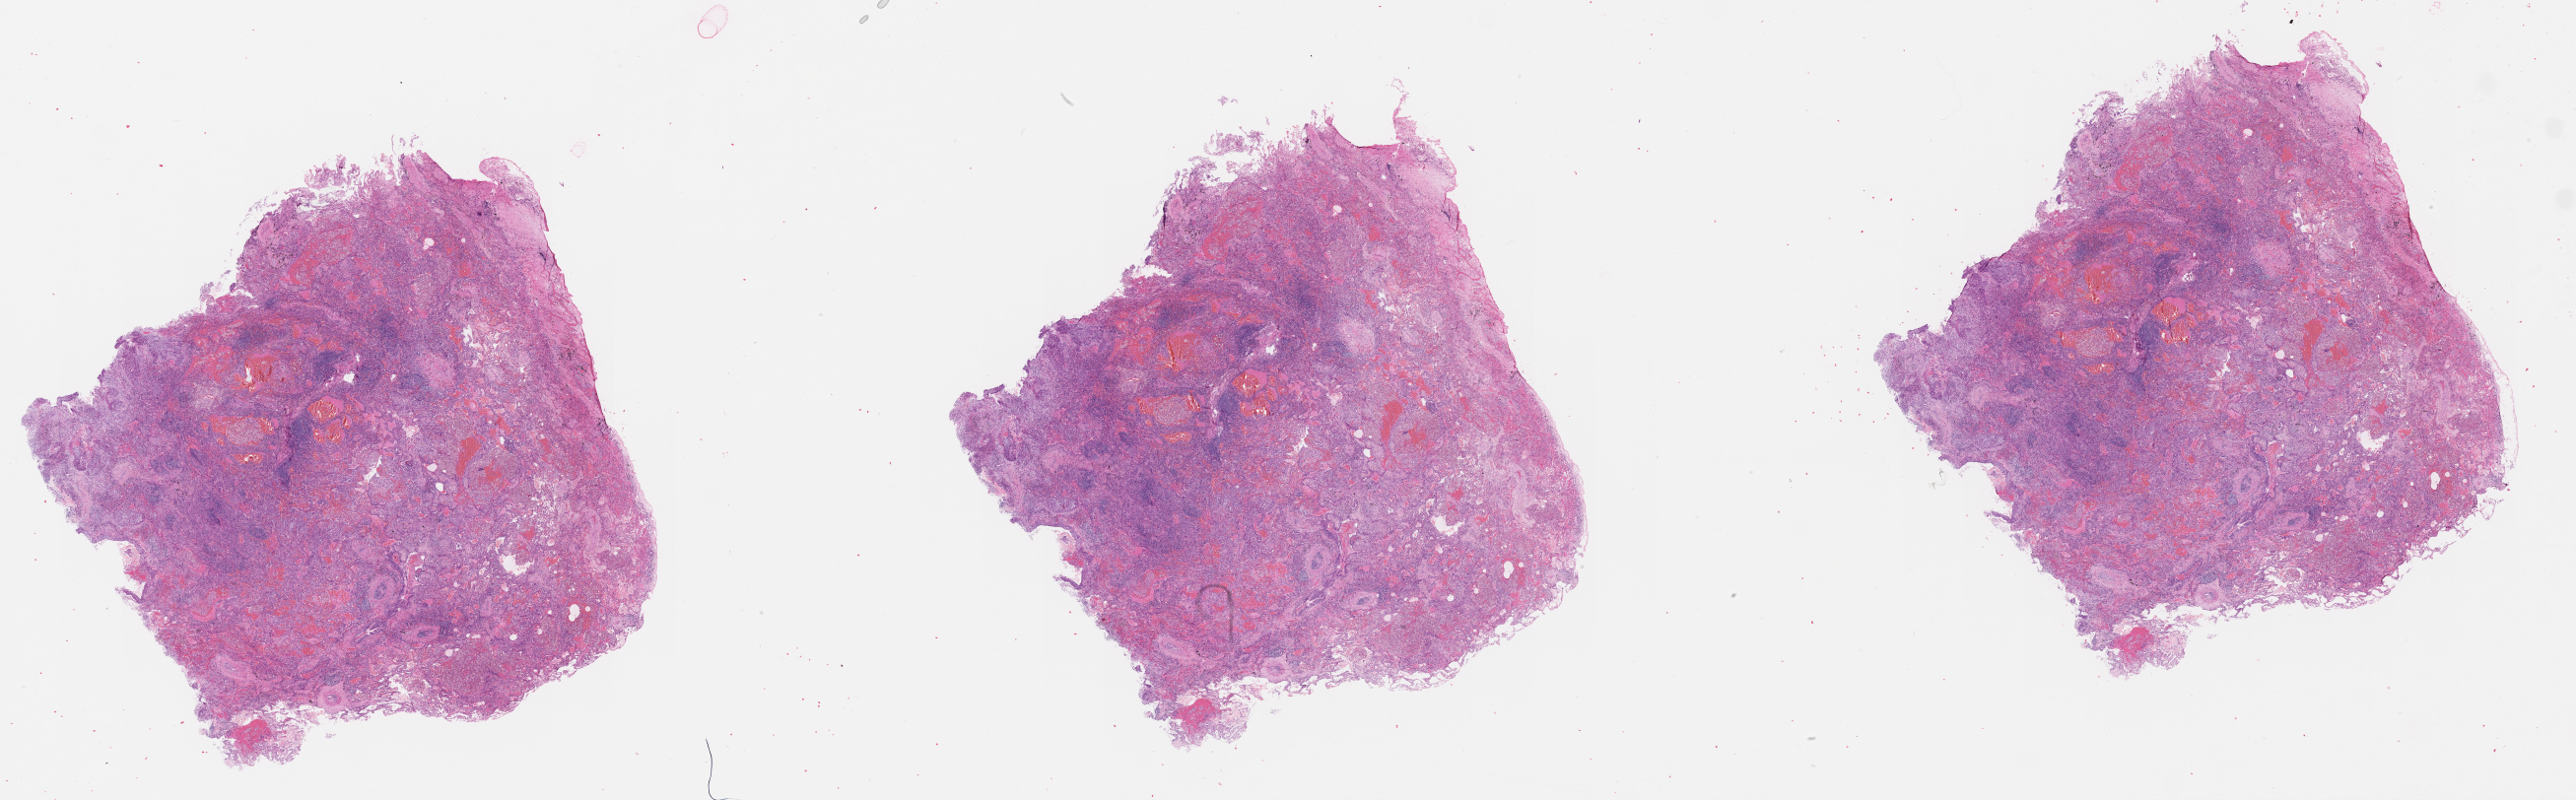
Digitized Hematoxylin and eosin (H&E) stained tissue section (whole slide), a low-resolution overview of the entire scanned area, about 42.1 x 13.1 mm, tumour tissue sample, lung. Patient: male, age 57 years.
Patient diagnosis (cohort enrolment): squamous cell carcinoma (lung).